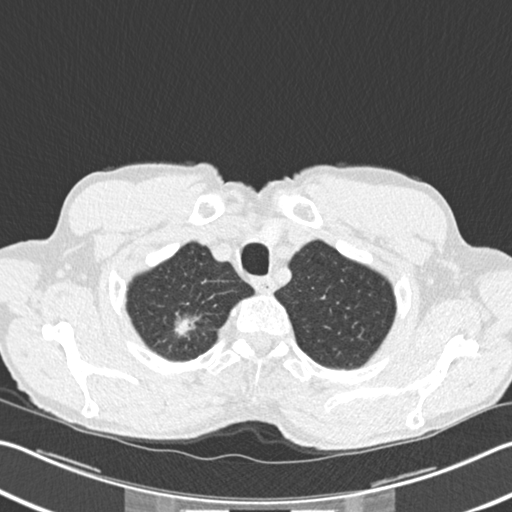
Chest CT (low-dose screening protocol), one axial image; second annual screen; lung window (W 1500 / L -600 HU); 120 kVp. Male, age 62 years at enrolment. Former smoker at enrolment.
Expert reader's lesion annotation, bounding box [x1, y1, x2, y2] px = [163, 303, 207, 347]. The screening reader recorded 2 non-calcified nodules or masses ≥4 mm on this exam (right upper lobe, right upper lobe); which of them this box marks is not recorded. Official screen result: positive, change unspecified: nodule(s) >= 4 mm or enlarging nodule(s), mass(es), or other non-specific abnormalities suspicious for lung cancer. Lung cancer was diagnosed 5 days after this screen: bronchiolo-alveolar adenocarcinoma, NOS, right upper lobe, well differentiated (G1), stage IA (AJCC 6th edition), 15 mm at pathology.